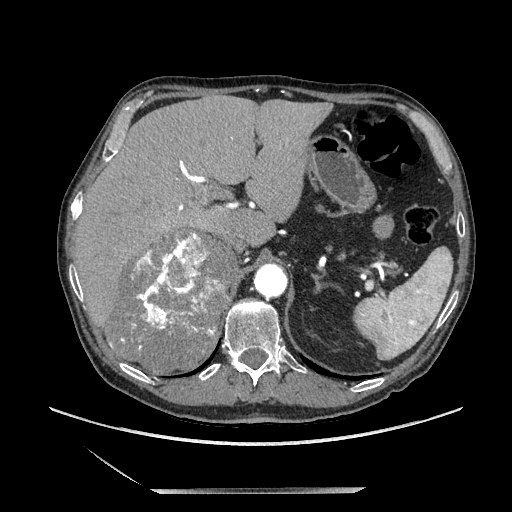
Contrast-enhanced abdominal CT, one axial slice. Position 149 of 243 along the scan axis. Soft-tissue window (W 400 / L 40 HU). 1.25 mm slice thickness. 512 × 512 image matrix, field of view 420 × 420 mm. Male patient. From the clinical record (not read from this slice): diagnosis: adrenocortical carcinoma; tumour side: right adrenal; tumour size at pathology: 16 cm; Ki-67 index: 17 %; stage (as recorded): 3.
Outlined on this slice (semi-automatic segmentation, software-assisted and operator-edited):
- mass: bounding box [x1, y1, x2, y2] px = [108, 232, 239, 373]